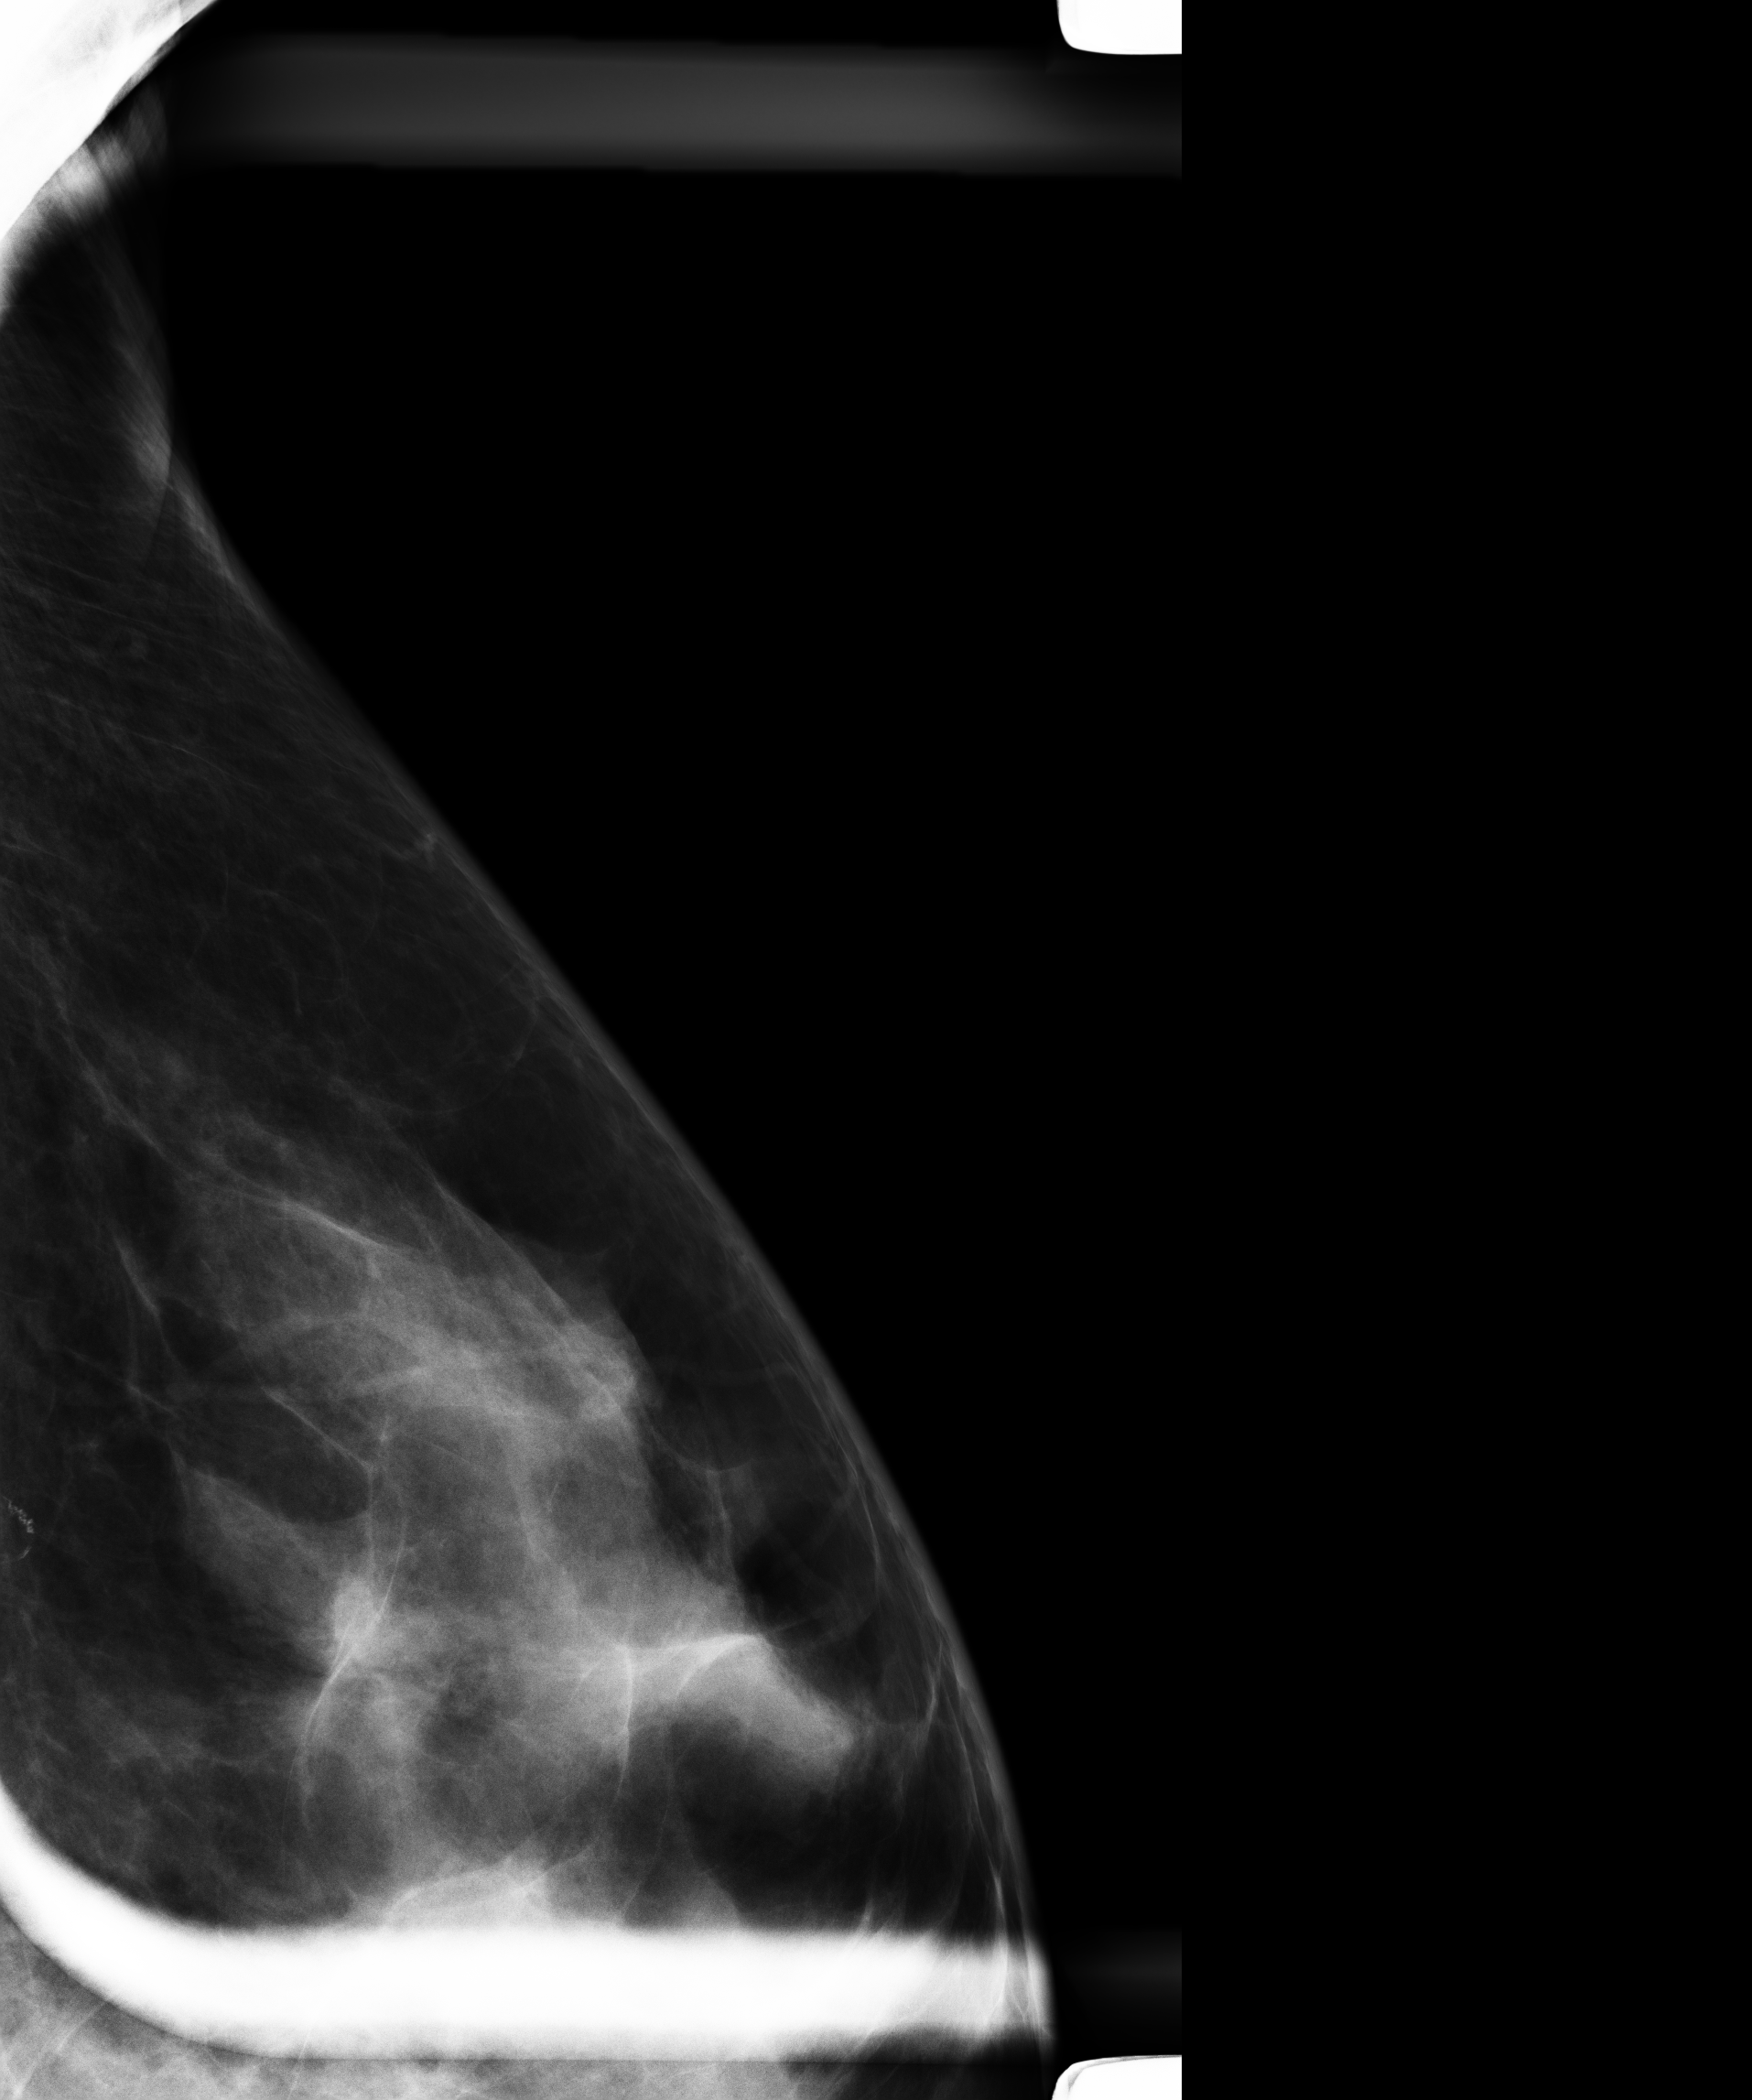
Full-field digital mammogram (FFDM); left breast; exaggerated CC view (lateral); diagnostic examination (additional views); compressed breast thickness 38 mm. Patient: female, 54 years.
BI-RADS breast density category at the screening exam (both breasts, scale 1–4): 3. Final BI-RADS category for the screening round (tomosynthesis exam, both breasts): category 3. Recall: recalled for additional imaging after this screen.